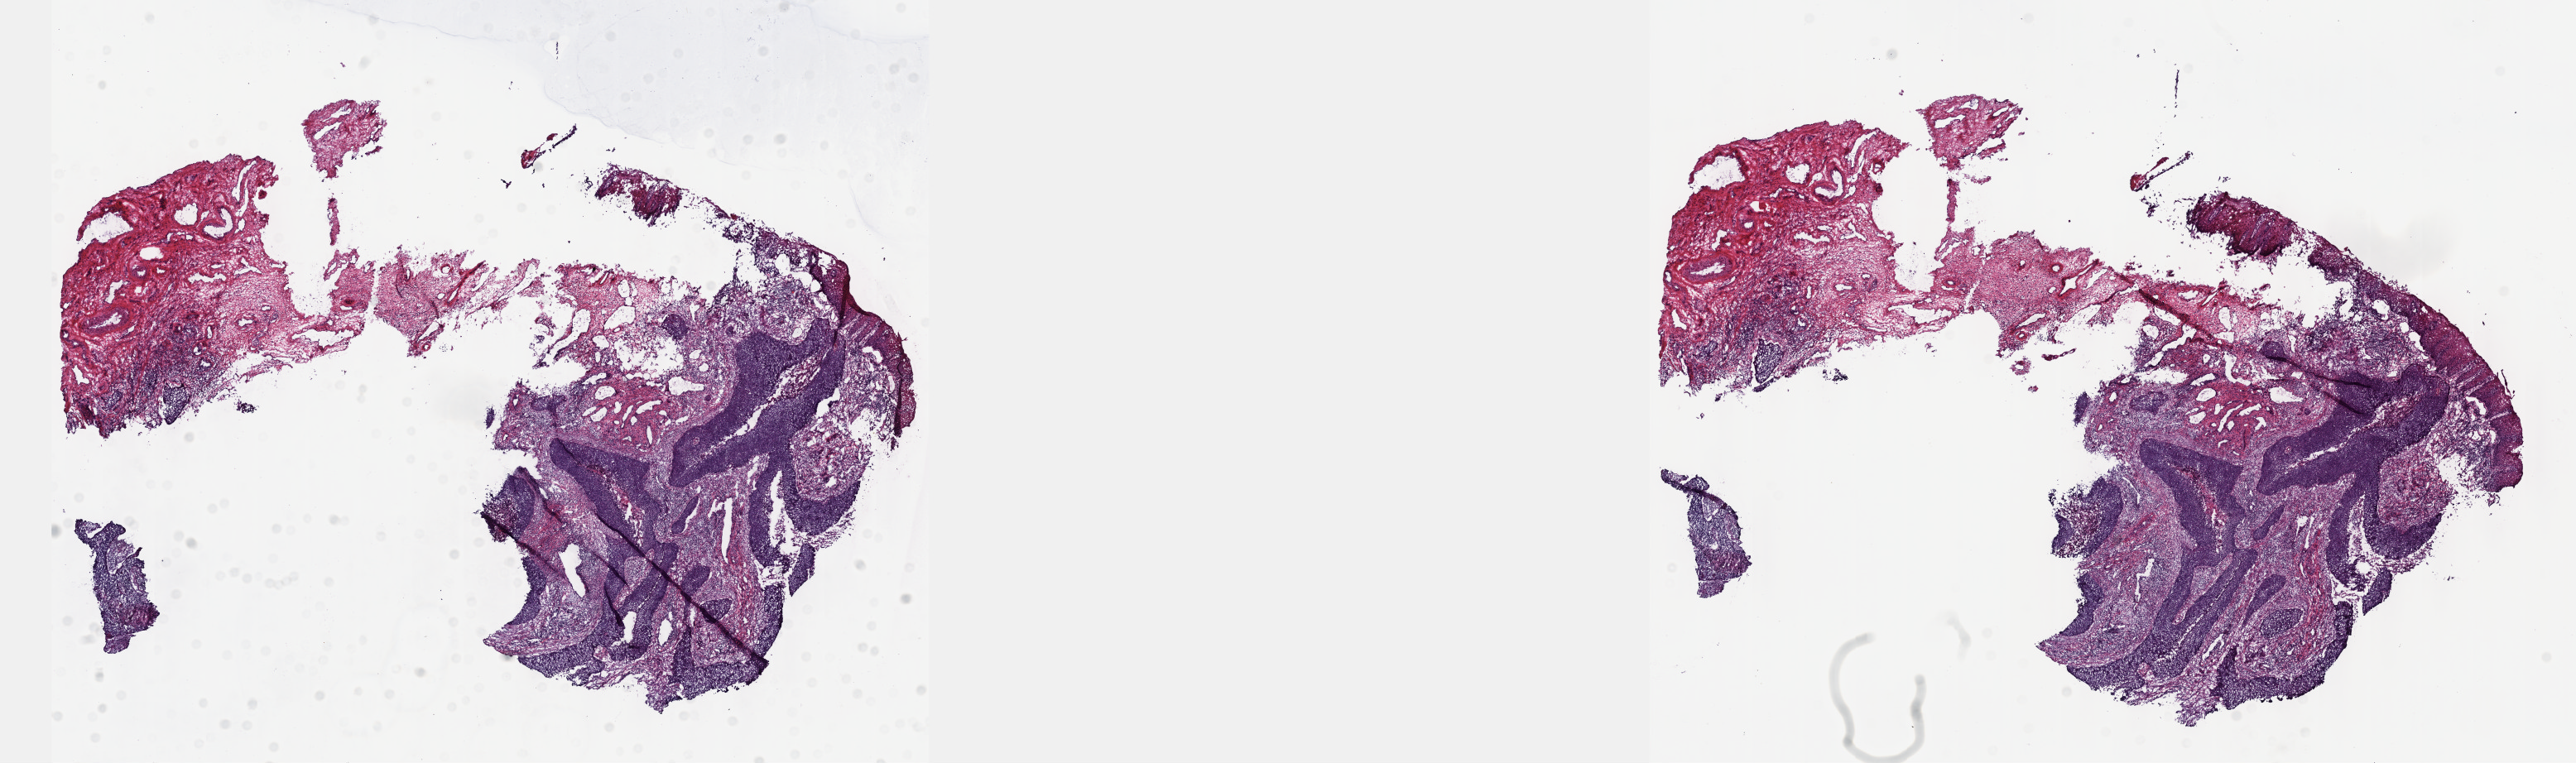
Digitized H&E-stained tissue section (whole slide), shown as a low-resolution overview of the whole scanned area (about 25.1 x 7.5 mm, slide scanned at 40x); frozen section from the top of the tissue portion; primary tumour sample from the cervix. Female, age 38 years at initial diagnosis. Histologic grade: G2 (moderately differentiated). Slide review estimates, as recorded: tumour cells 60%, tumour nuclei 60%, normal cells 0%, stromal cells 30%, necrosis 10%. Inflammatory infiltration, as recorded: lymphocyte infiltration 40%, monocyte infiltration 20%, neutrophil infiltration 20%.
* diagnosis: Squamous cell carcinoma, NOS (cervix uteri)
* FIGO stage: IB2
* lymph nodes positive (case pathology): 0 of 10 examined